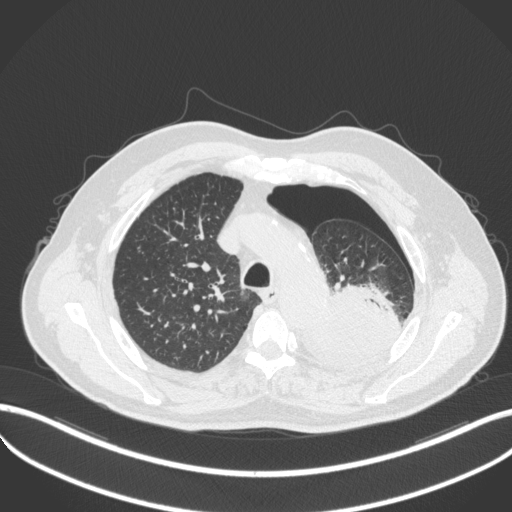
Chest CT, one axial slice; slice 383 of 466 in the series (ordered by position); 120 kVp; lung window (W 1500 / L -600 HU); 1 mm slice thickness; 512 × 512 image matrix, field of view 400 × 400 mm. Male patient, age 76 years. From the clinical record (not read from this slice): clinical TNM (as recorded): T3 N0 M1b.
Outlined on this slice (rectangle marked by the reading radiologist):
- lung tumour (recorded histology: adenocarcinoma): box from (x=303, y=275) to (x=403, y=375) px